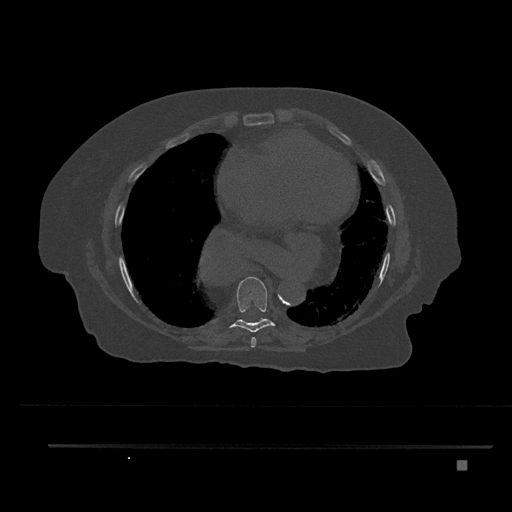
CT including the spine, one axial slice. Position 442 of 797 along the scan axis. Bone window (W 1800 / L 400 HU). 0.5 mm slice thickness. 512 × 512 image matrix. Female patient, age 76 years. From the clinical record (not read from this slice): primary cancer: lung.
Outlined on this slice (semi-automatic segmentation, software-assisted and operator-edited):
- T7 vertebra: bounding box <251,337,256,348> (left, top, right, bottom; pixels)
- T8 vertebra: <228,277,276,332>